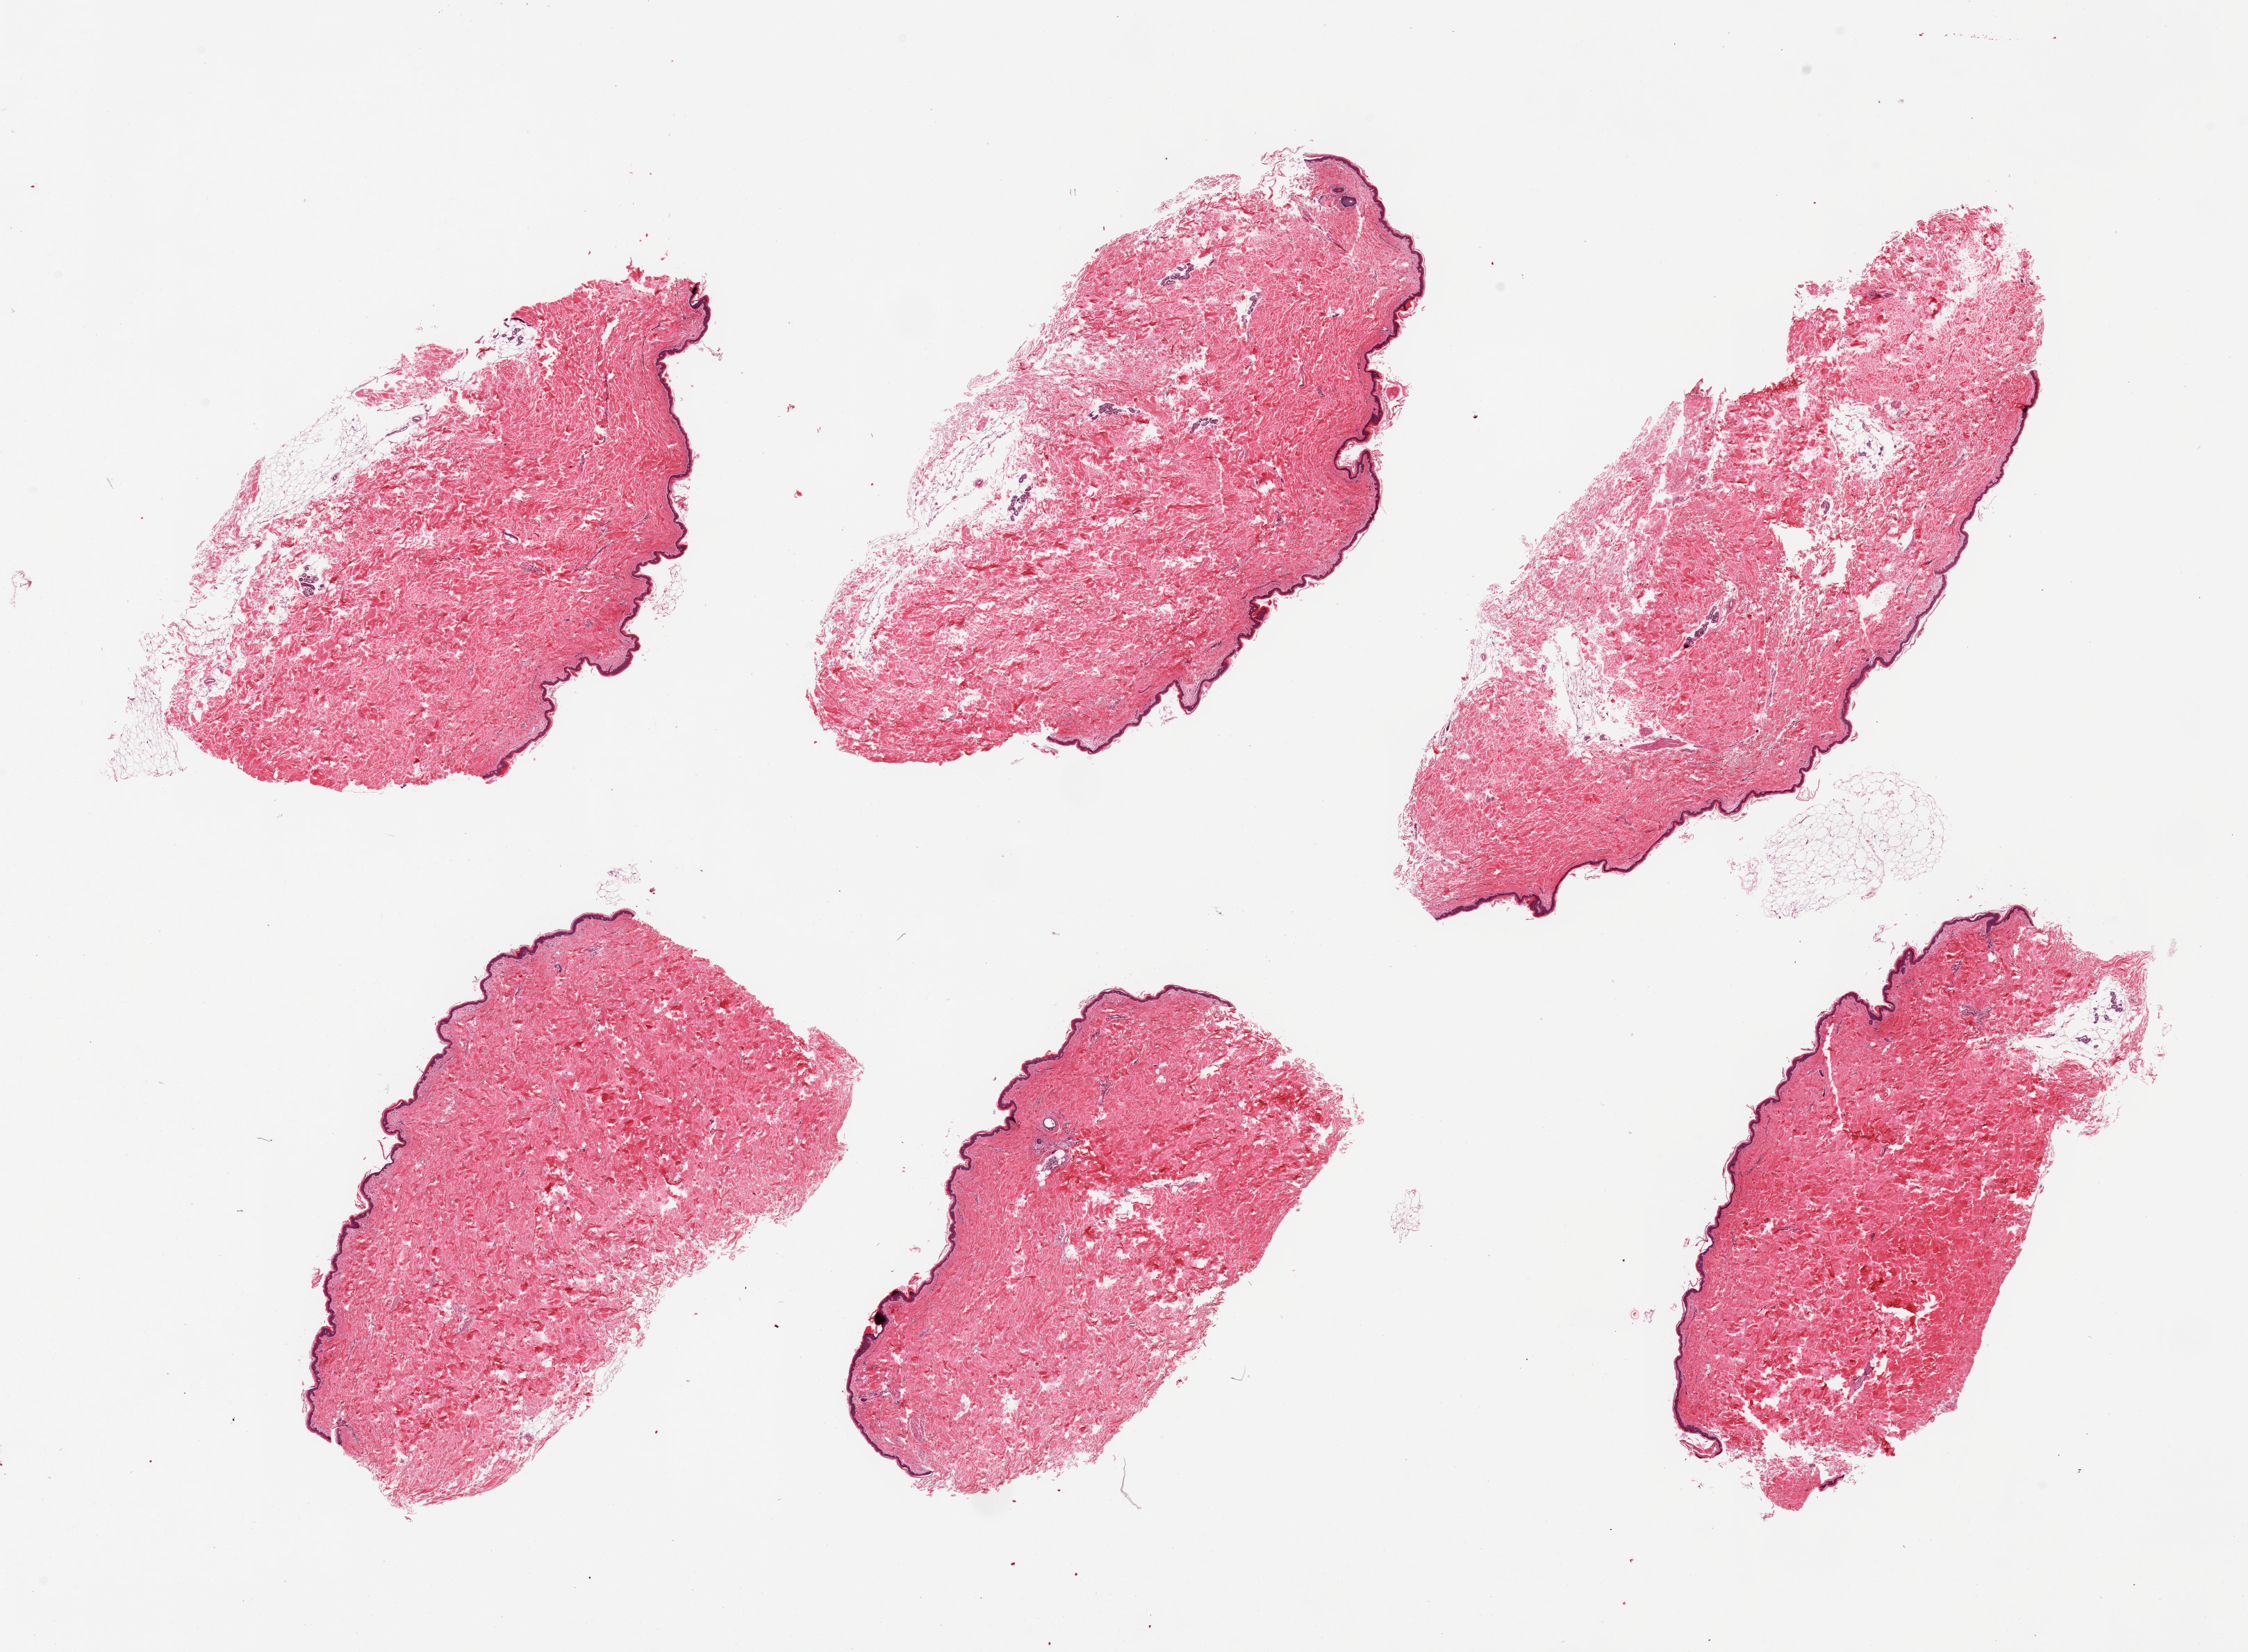
Digitized hematoxylin and eosin (H&E)-stained section, brightfield — whole scanned area (about 25.6 x 18.8 mm) shown as a low-resolution overview. PAXgene-fixed, paraffin-embedded tissue. Target tissue: skin of suprapubic region. Donor tissue sample. Female donor.
Pathologist's review note for this sample: 6 pieces; well trimmed; 5-20% dermal fat.